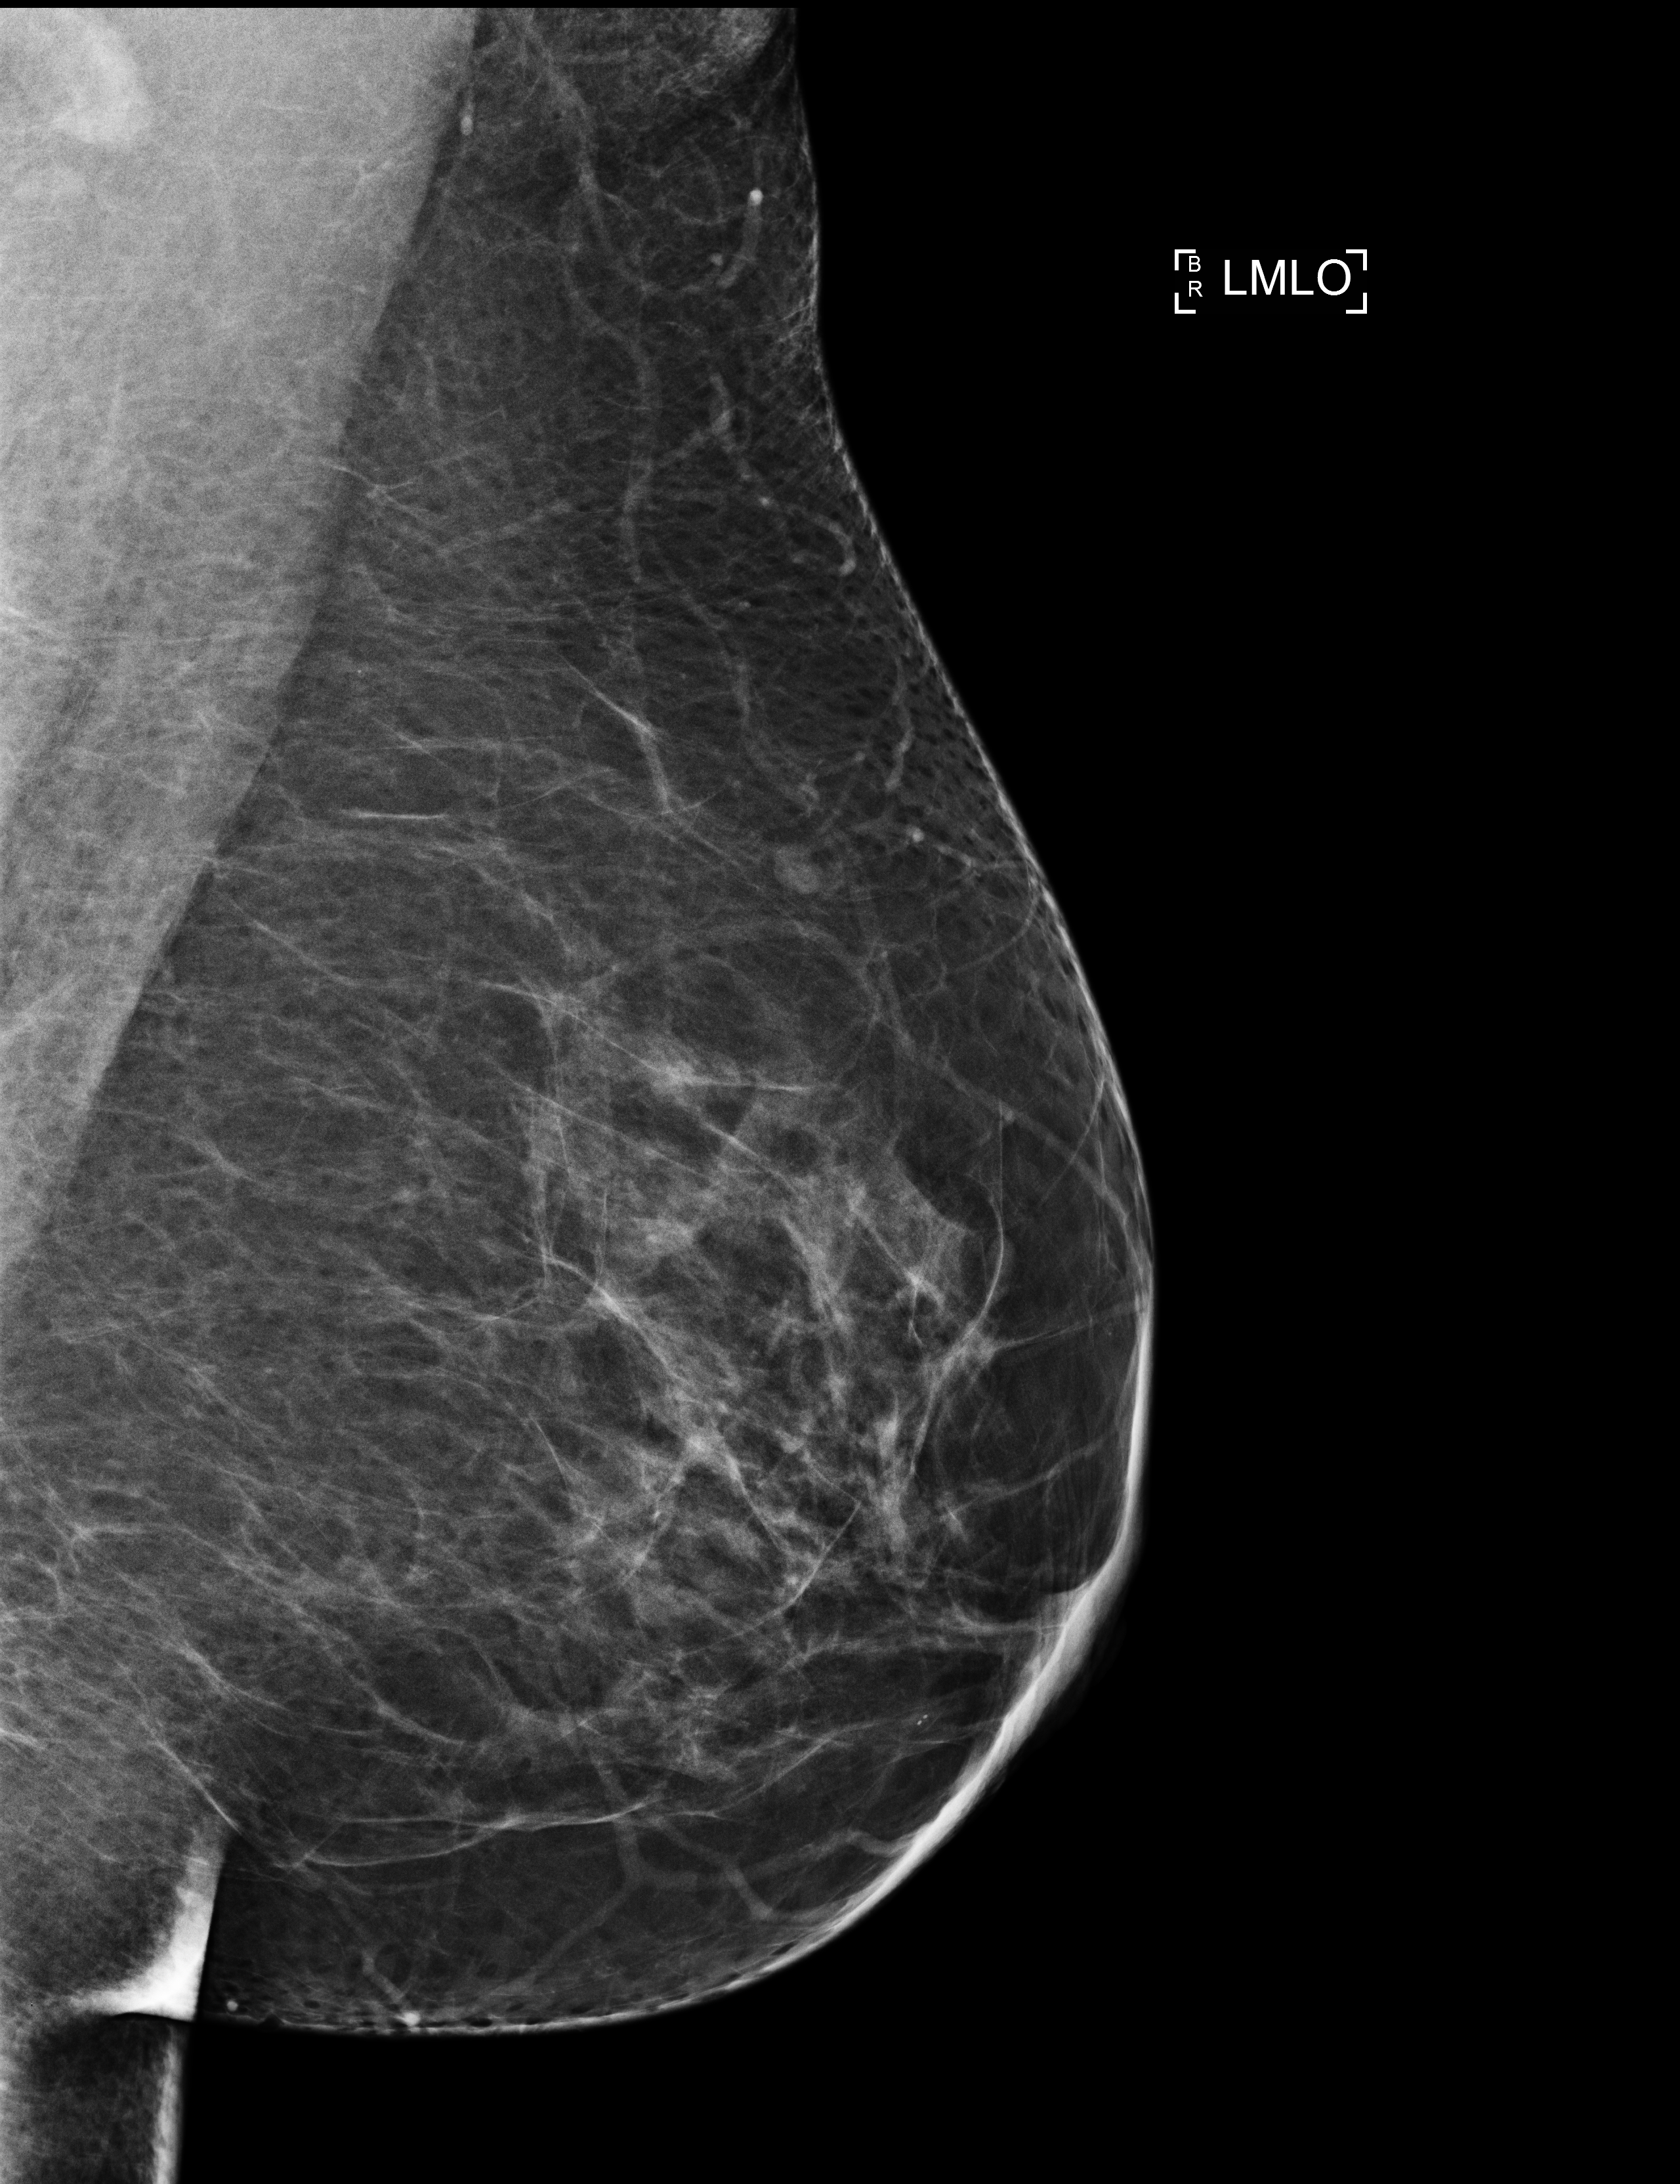
Full-field digital mammogram (FFDM), left breast, medio-lateral oblique projection, screening examination, compressed breast thickness 106 mm. Female patient, age 44 years.
Breast density at the screening exam (both breasts): scattered fibroglandular densities (BI-RADS density category b). Final BI-RADS category for the screening round (tomosynthesis exam, both breasts): category 2. Recall: no recall after this screen.